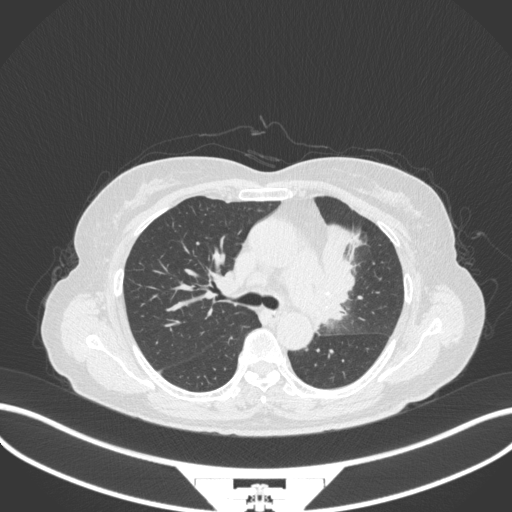
Chest CT, one axial slice; position 217 of 382 along the scan axis; reconstruction kernel B31f; lung window (W 1500 / L -600 HU); 512 × 512 image matrix. Female patient, age 64 years. Case-level facts recorded for this patient, not image findings: clinical TNM (as recorded): T2a N2 M0.
Outlined on this slice (rectangle marked by the reading radiologist):
- lung tumour (recorded histology: adenocarcinoma): bounding box [x1, y1, x2, y2] px = [315, 222, 362, 325]